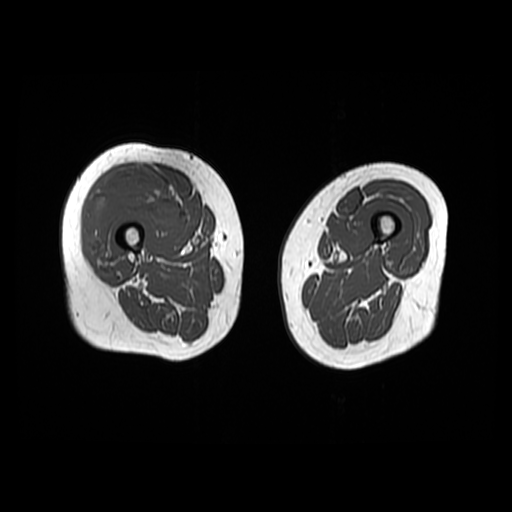
MRI of an extremity soft-tissue mass, one axial slice. Position 20 of 48 along the scan axis. 6 mm slice thickness. 512 × 512 image matrix. Female patient. From the clinical record (not read from this slice): histological type: pleiomorphic undifferentiated sarcoma; grade: high; site of the primary tumour: right quadricep.
Structures marked on this image (outlined manually by an expert reader):
- gross tumour volume including surrounding oedema: bounding box [x1, y1, x2, y2] px = [86, 169, 178, 266]
- gross tumour volume (mass): [86, 169, 178, 266]